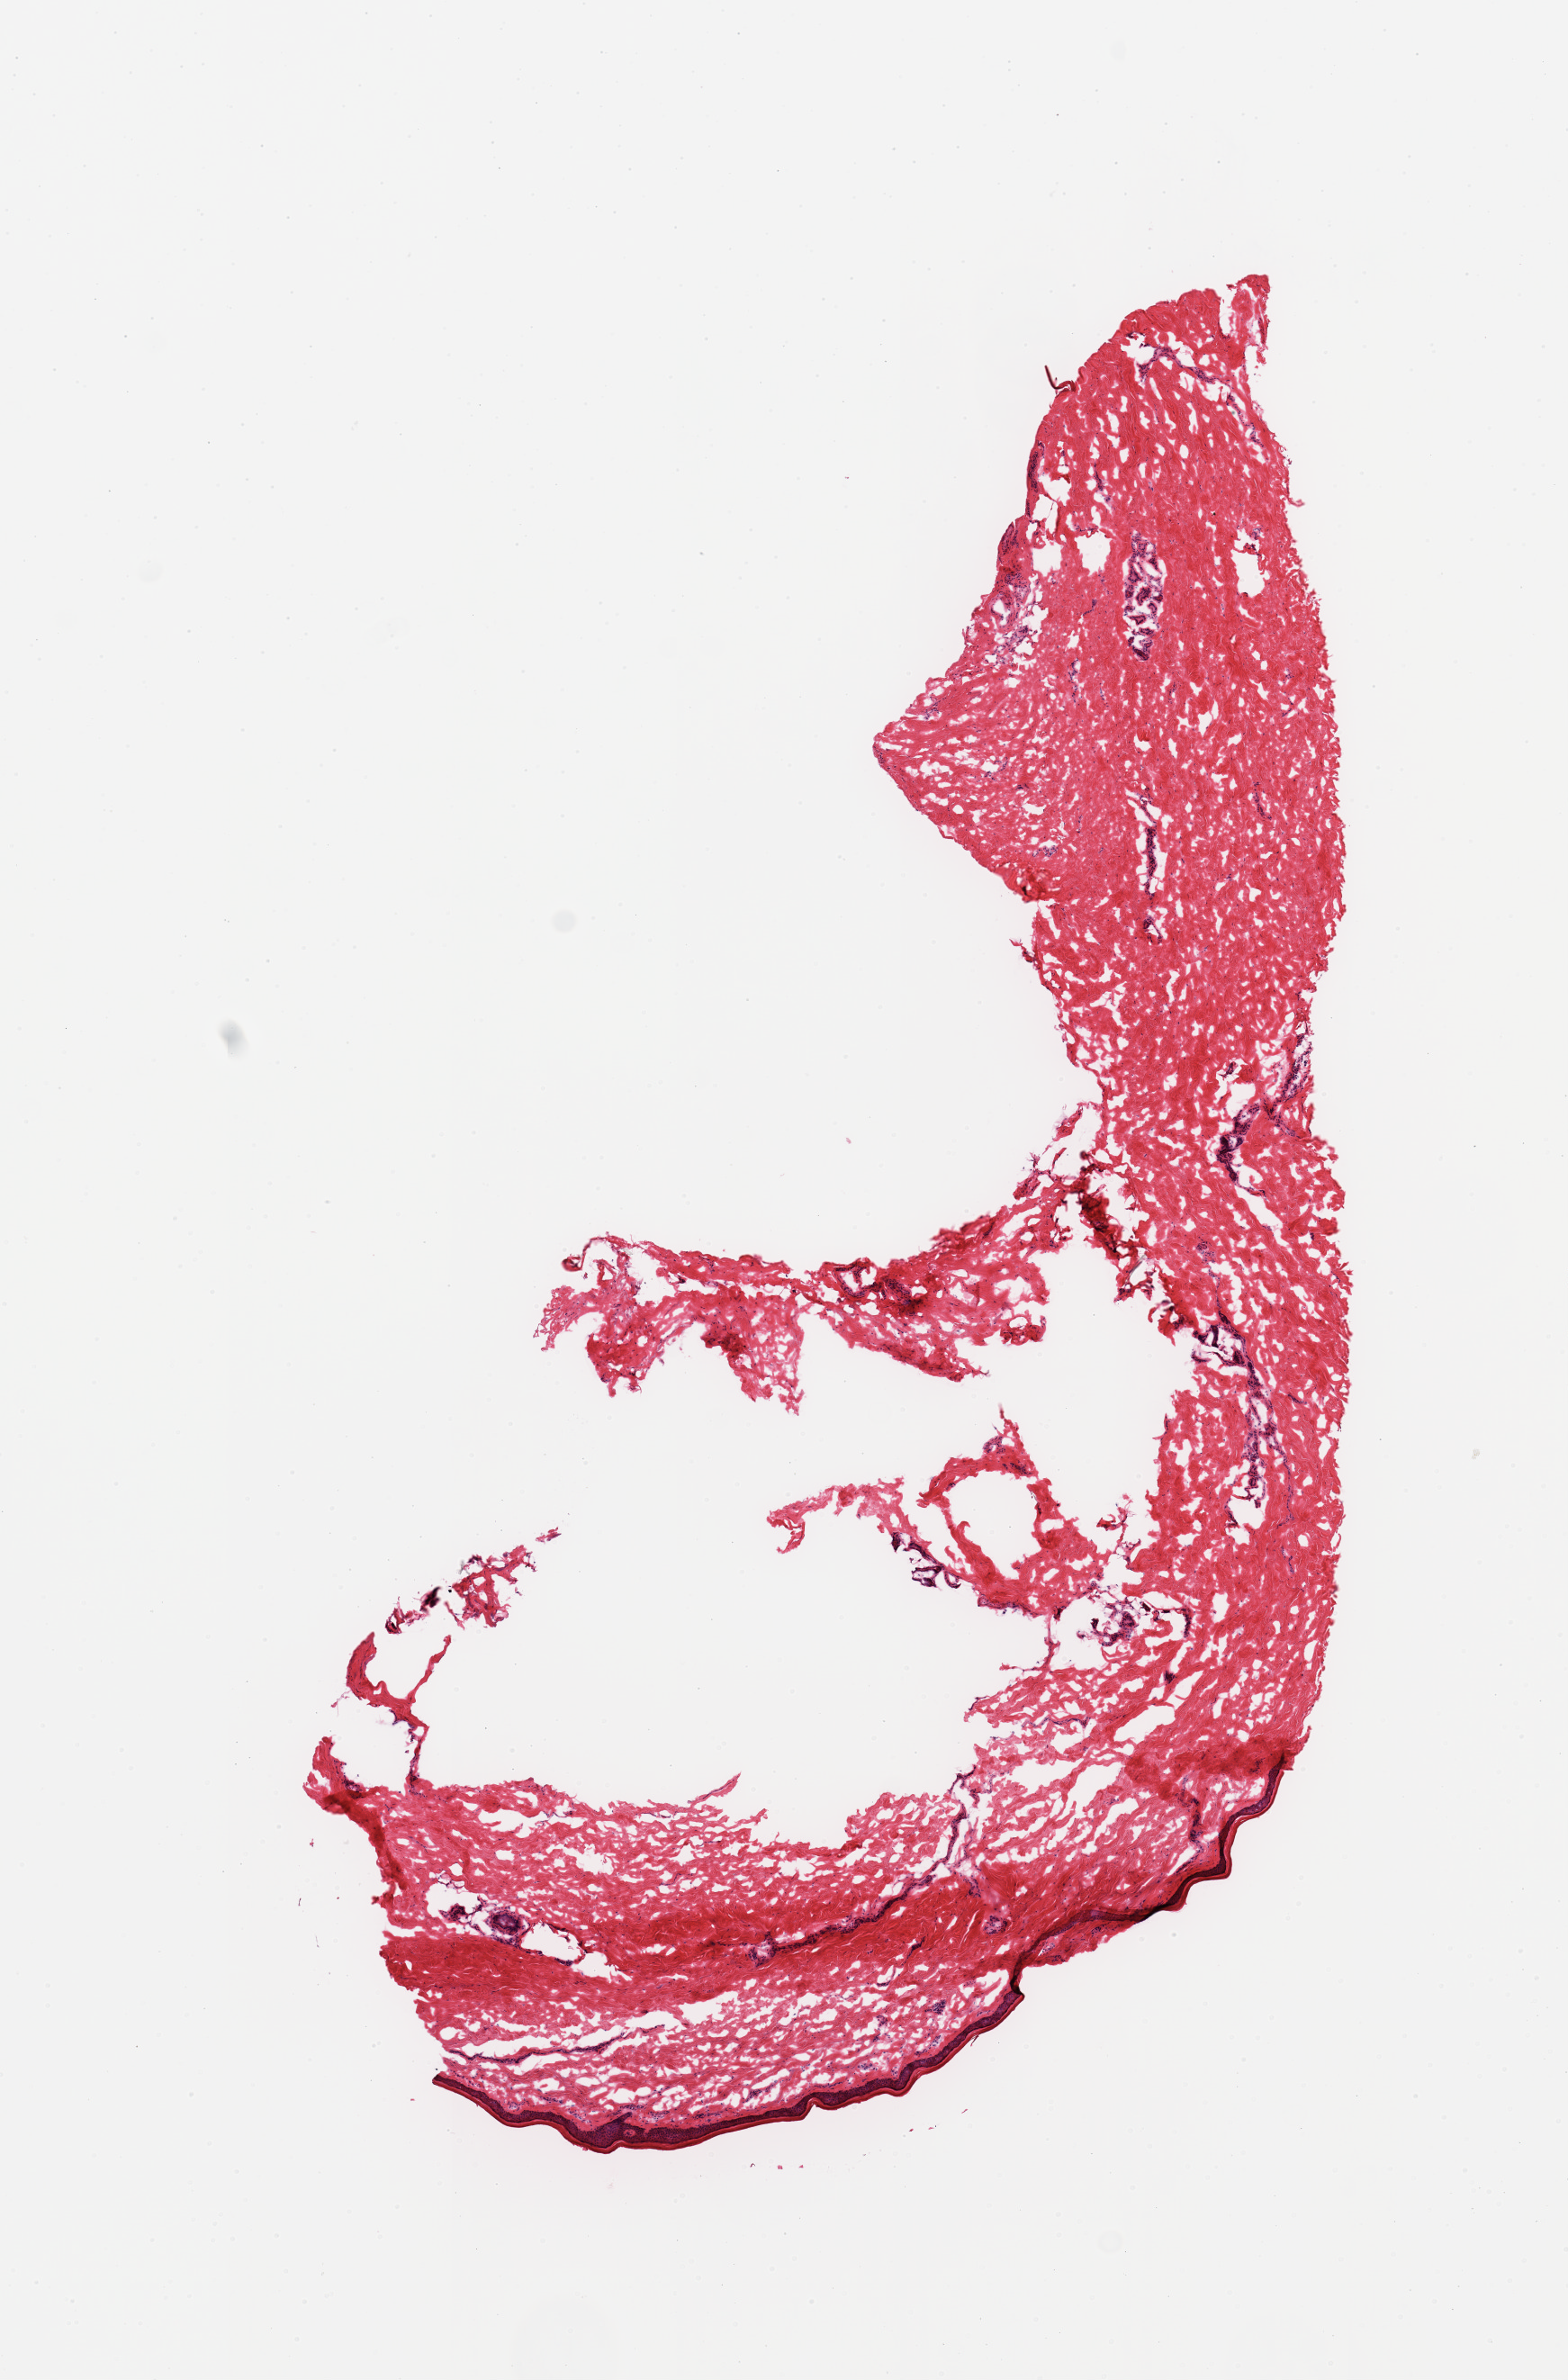
Hematoxylin and eosin (H&E) whole-slide image — shown as a low-resolution overview of the whole scanned area (about 6.9 x 10.5 mm). Frozen section. Sampled site (target tissue): skin of lower leg. Donor tissue sample.
• pathologist's review note for this sample: 1 piece